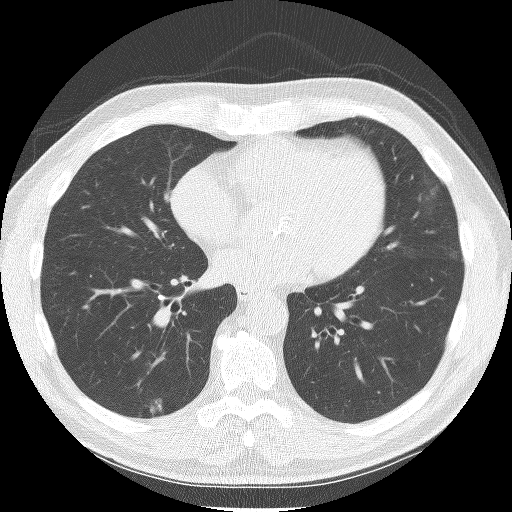
Axial slice from a low-dose chest CT screening exam; baseline screening round; lung window (W 1500 / L -600 HU); 2.5 mm slice thickness; lung (sharp) reconstruction kernel (BONE); 120 kVp; slice 85 of 150 in the series; 512 × 512 image matrix. Male participant, aged 61 years at enrolment.
Lesion marked by an expert reader, box from (x=128, y=387) to (x=178, y=425) px. Screening reader's record for this exam (one nodule recorded; not confirmed to be the boxed lesion): non-calcified nodule or mass ≥4 mm, right lower lobe, 12 × 11 mm, spiculated (stellate) margins, soft tissue attenuation.